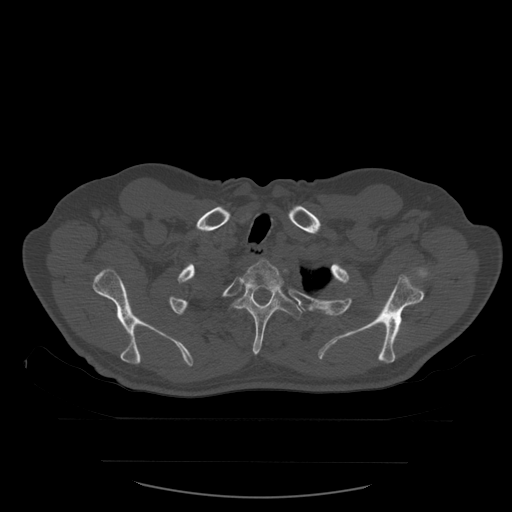
CT including the spine, one axial slice. Bone window (W 1800 / L 400 HU). 1.25 mm slice thickness. 512 × 512 image matrix. Patient age 71 years. Case-level facts recorded for this patient, not image findings: primary cancer: lung; vertebrae with lytic lesions (as recorded): T1, T2, L5, S1.
Outlined on this slice (semi-automatically segmented with operator editing):
- T2 vertebra: bounding box [x1, y1, x2, y2] px = [242, 260, 285, 290]
- T3 vertebra: [227, 289, 303, 356]